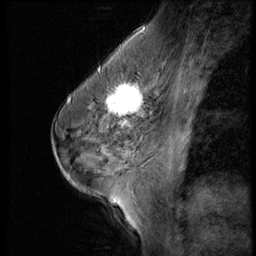
Breast MRI (dynamic contrast-enhanced), one sagittal slice; position 35 of 56 along the scan axis; 3 images stored at this slice position (order not interpretable as contrast timing); 1.5 T; TE 4.2 ms, TR 9 ms; 256 × 256 image matrix. Patient: female, 45 years. From the clinical record (not read from this slice): setting: breast cancer imaged before/during neoadjuvant chemotherapy; receptor status: HR-positive, HER2-negative.
Structures marked on this image (semi-automatic segmentation, software-assisted and operator-edited):
- analysis volume of interest (the breast-tissue region the enhancement analysis was run in; not a lesion): bounding box [x1, y1, x2, y2] px = [102, 77, 166, 129]
- tumour enhancement mask (voxels above the 140 % enhancement threshold inside the analysis volume of interest): [102, 82, 152, 129]